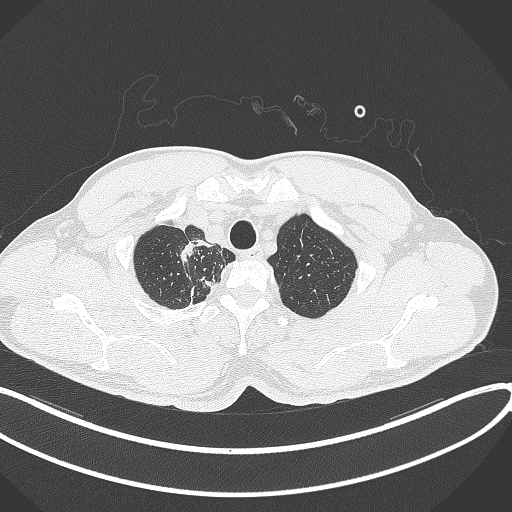
Chest CT, one axial slice. Slice 336 of 391 in the series (ordered by position). Reconstruction kernel B70f. Lung window (W 1500 / L -600 HU). 1 mm slice thickness. 512 × 512 image matrix, field of view 400 × 400 mm. Male patient, age 48 years. Case-level facts recorded for this patient, not image findings: clinical TNM (as recorded): T1c N1 M1.
Outlined on this slice (rectangle marked by the reading radiologist):
- lung tumour (recorded histology: adenocarcinoma): bounding box <175,239,198,271> (left, top, right, bottom; pixels)